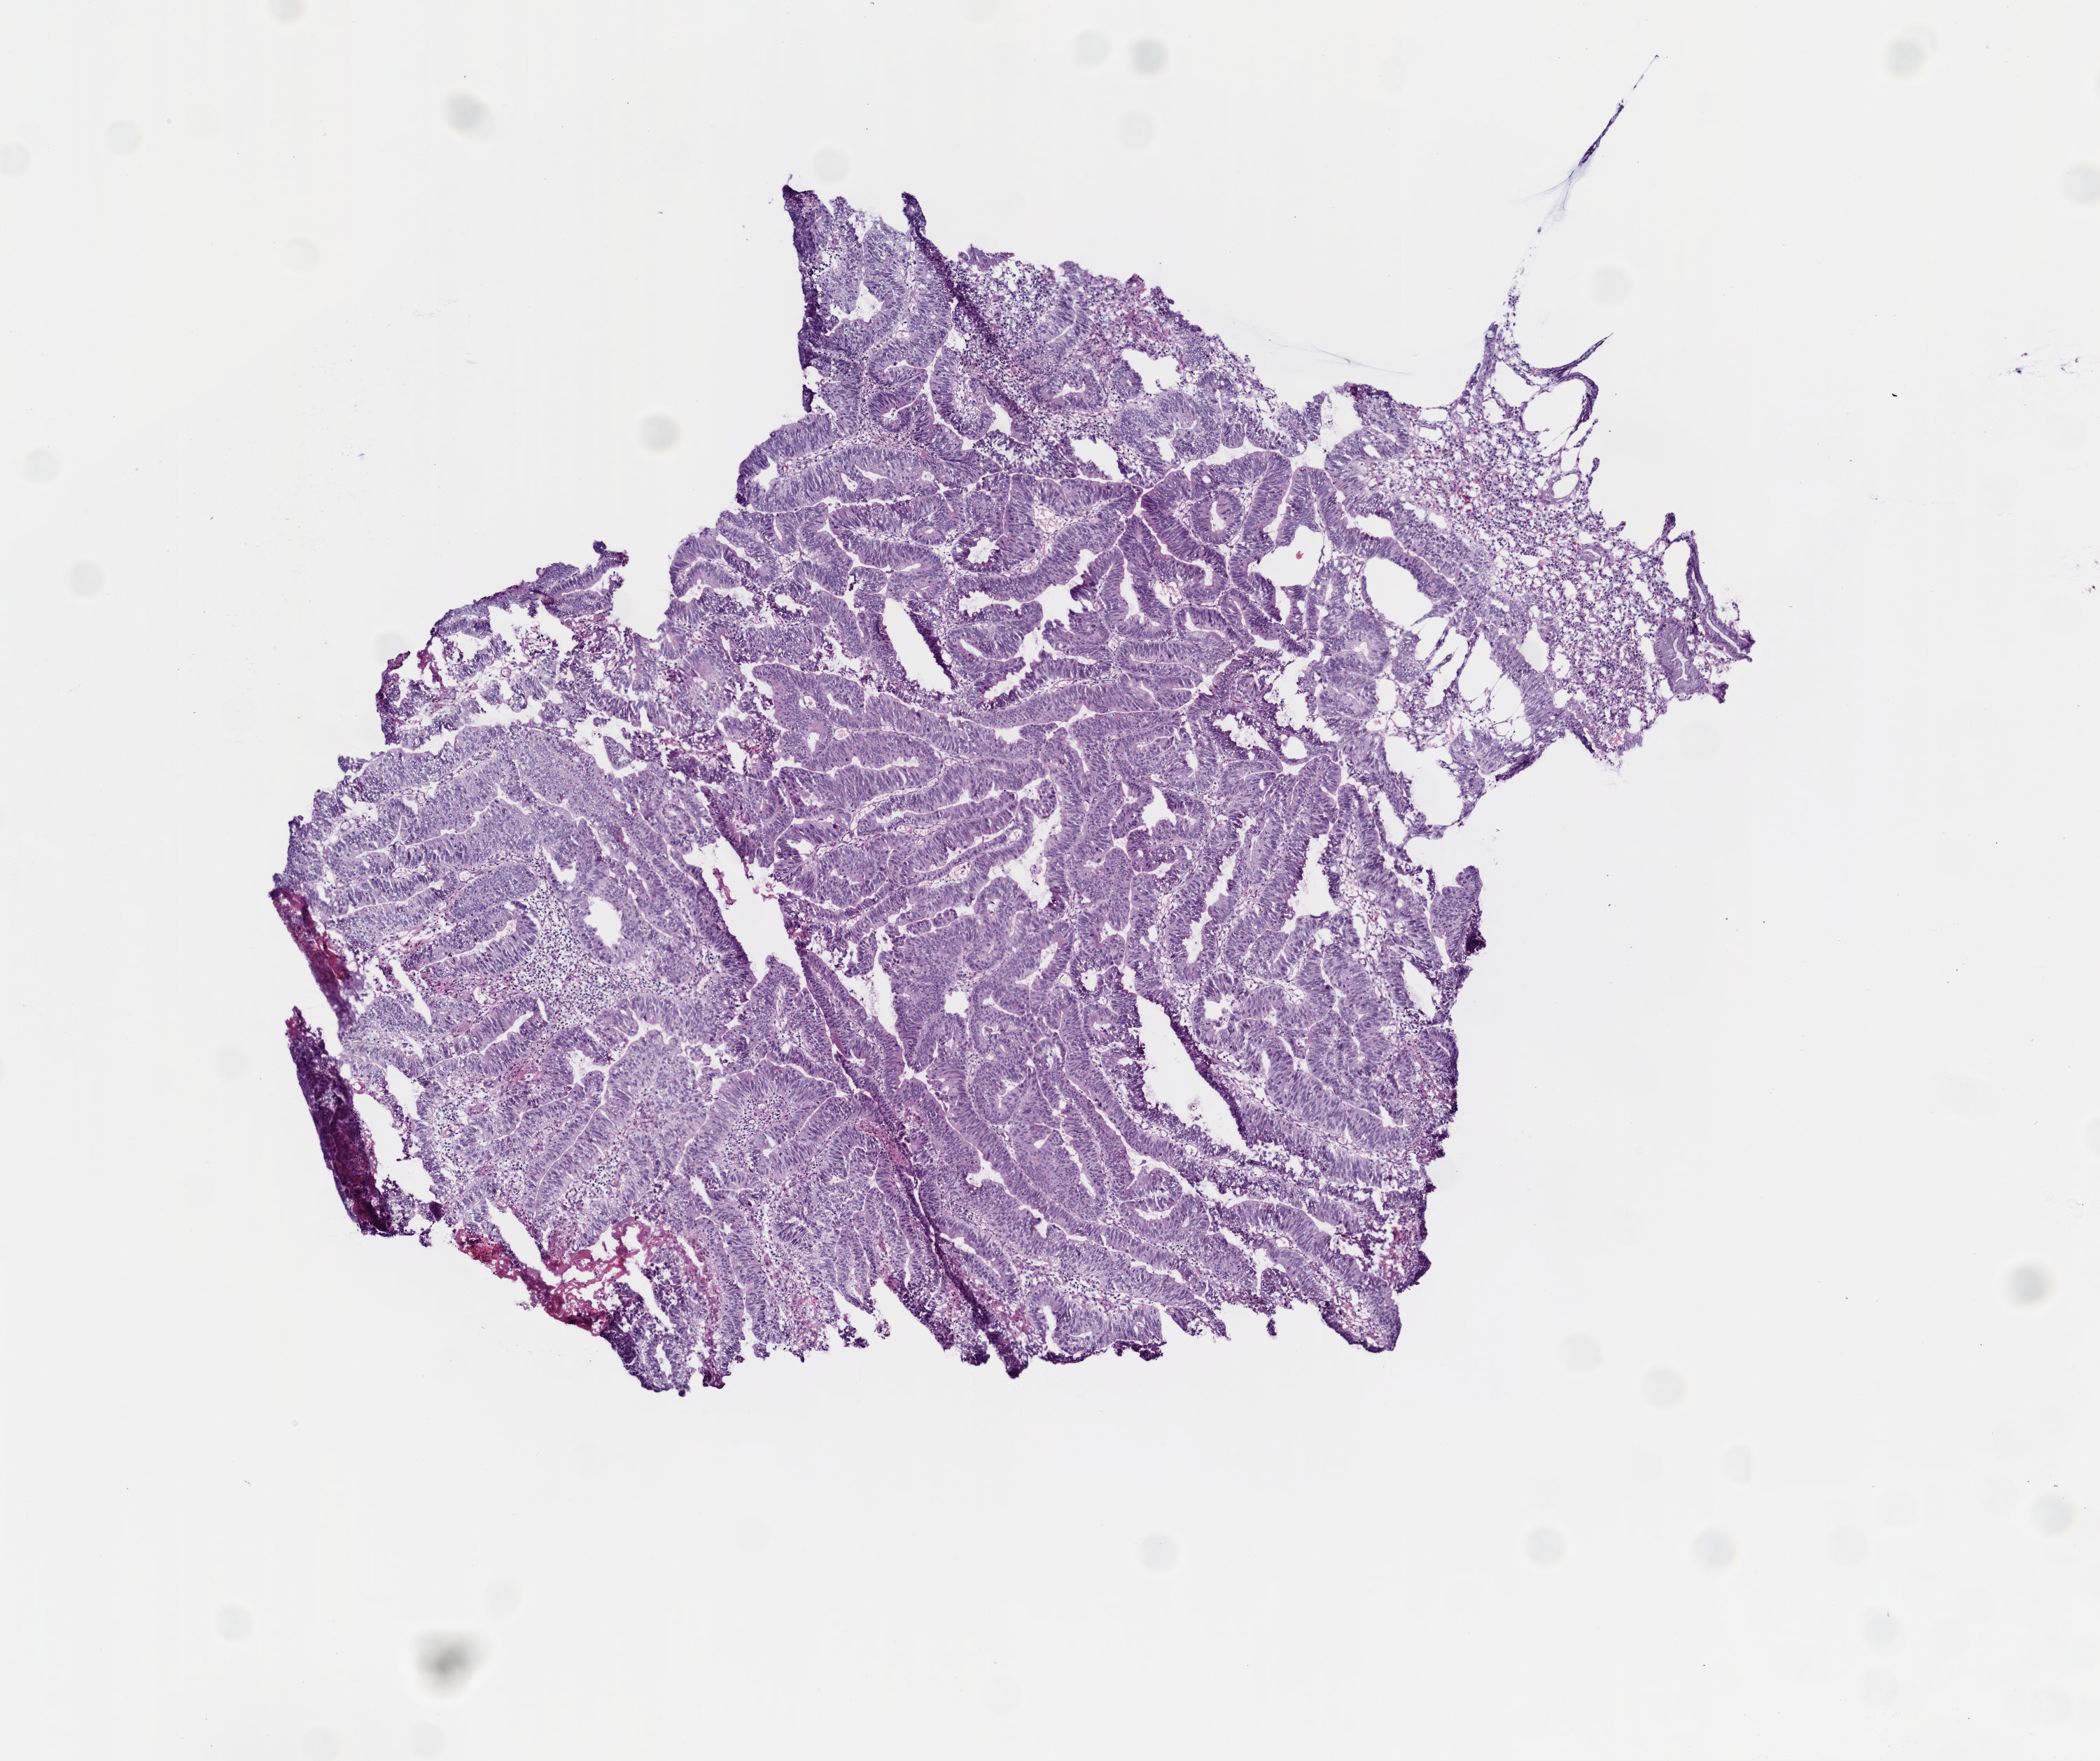
Whole-slide histology image, H&E — low-resolution overview of the scanned area, about 6.0 x 5.0 mm; frozen section from the top of the tissue portion; sample: primary tumour, colon. Male patient; age at initial diagnosis 55 years. Composition of this section per pathologist review: tumour cells 90%, tumour nuclei 70%, normal cells 0%, stromal cells 5%, necrosis 5%. Inflammatory infiltration, as recorded: lymphocyte infiltration 25%, monocyte infiltration 0%, neutrophil infiltration 0%.
Diagnosis: Adenocarcinoma, NOS. AJCC pathologic stage: IV (5th edition). TNM: T3 N0 M1. Lymph nodes positive (case pathology): 0 of 39 examined.